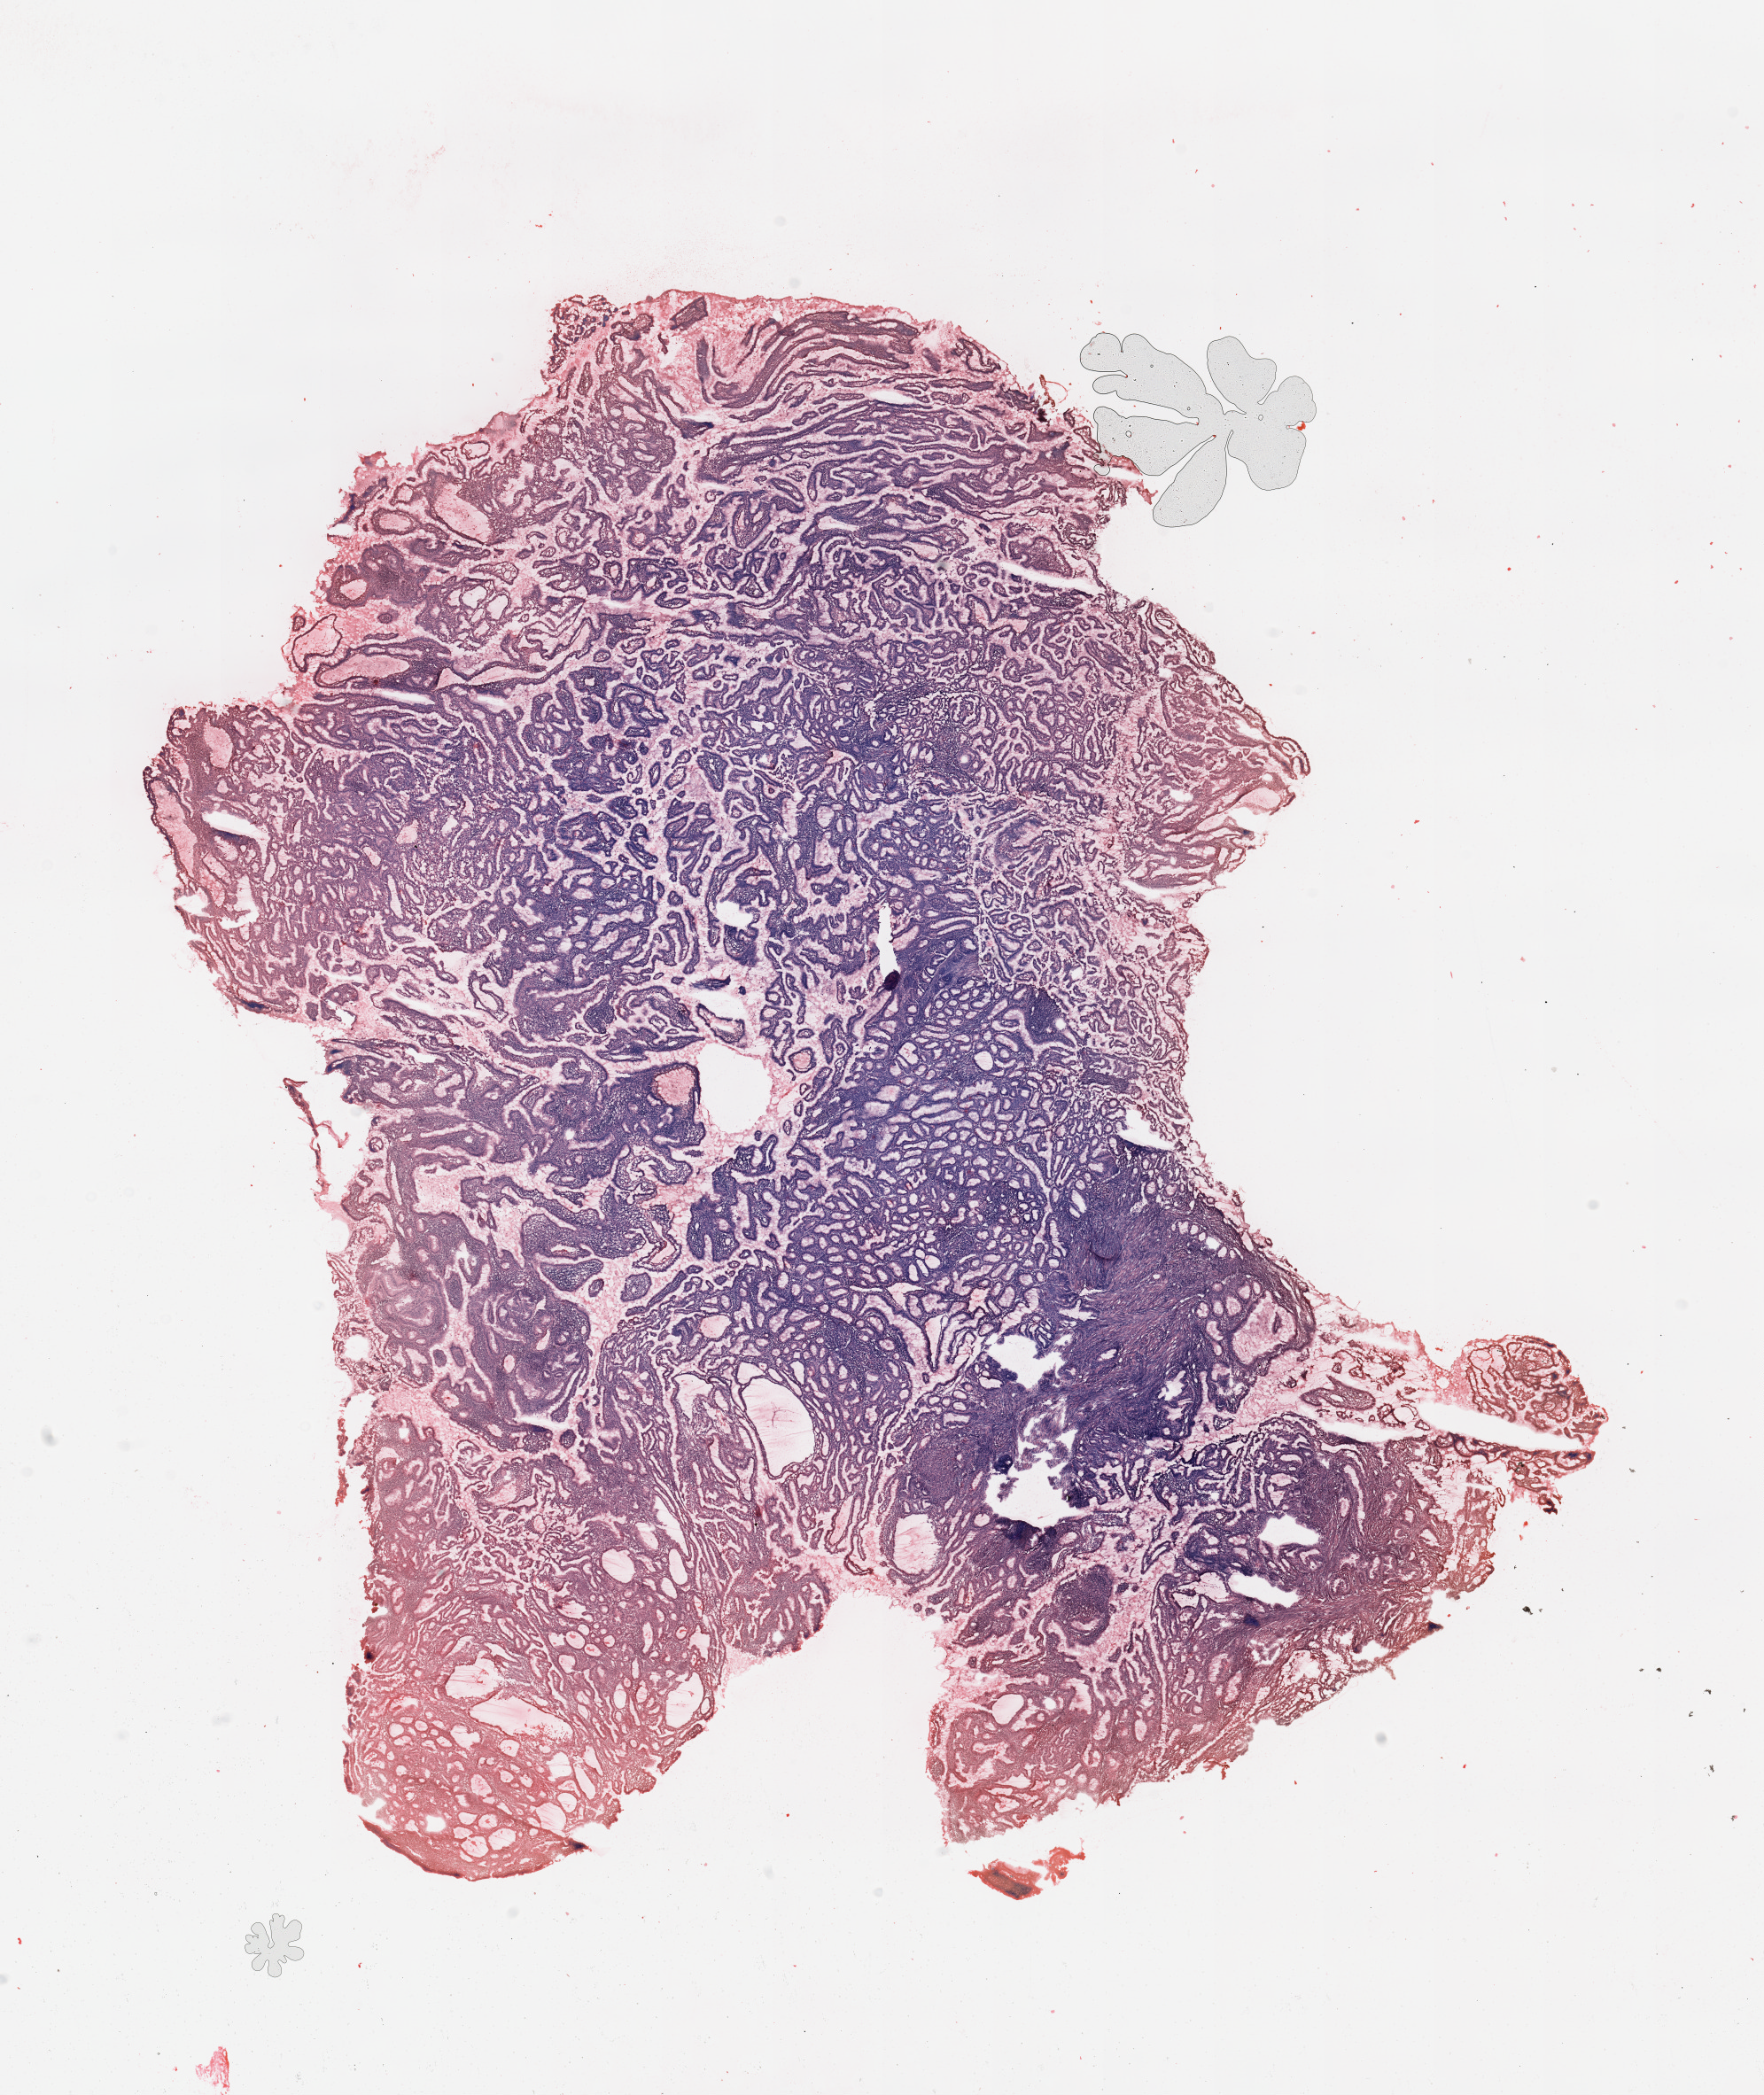
Hematoxylin and eosin (H&E) stained whole-slide image, a low-resolution overview of the entire scanned area, about 15.8 x 18.7 mm (slide scanned at 20x); uterus, tumour tissue. 61-year-old female patient. Histologic grade: G1 (well differentiated).
Diagnosis: Endometrioid adenocarcinoma, NOS. AJCC pathologic stage: I.